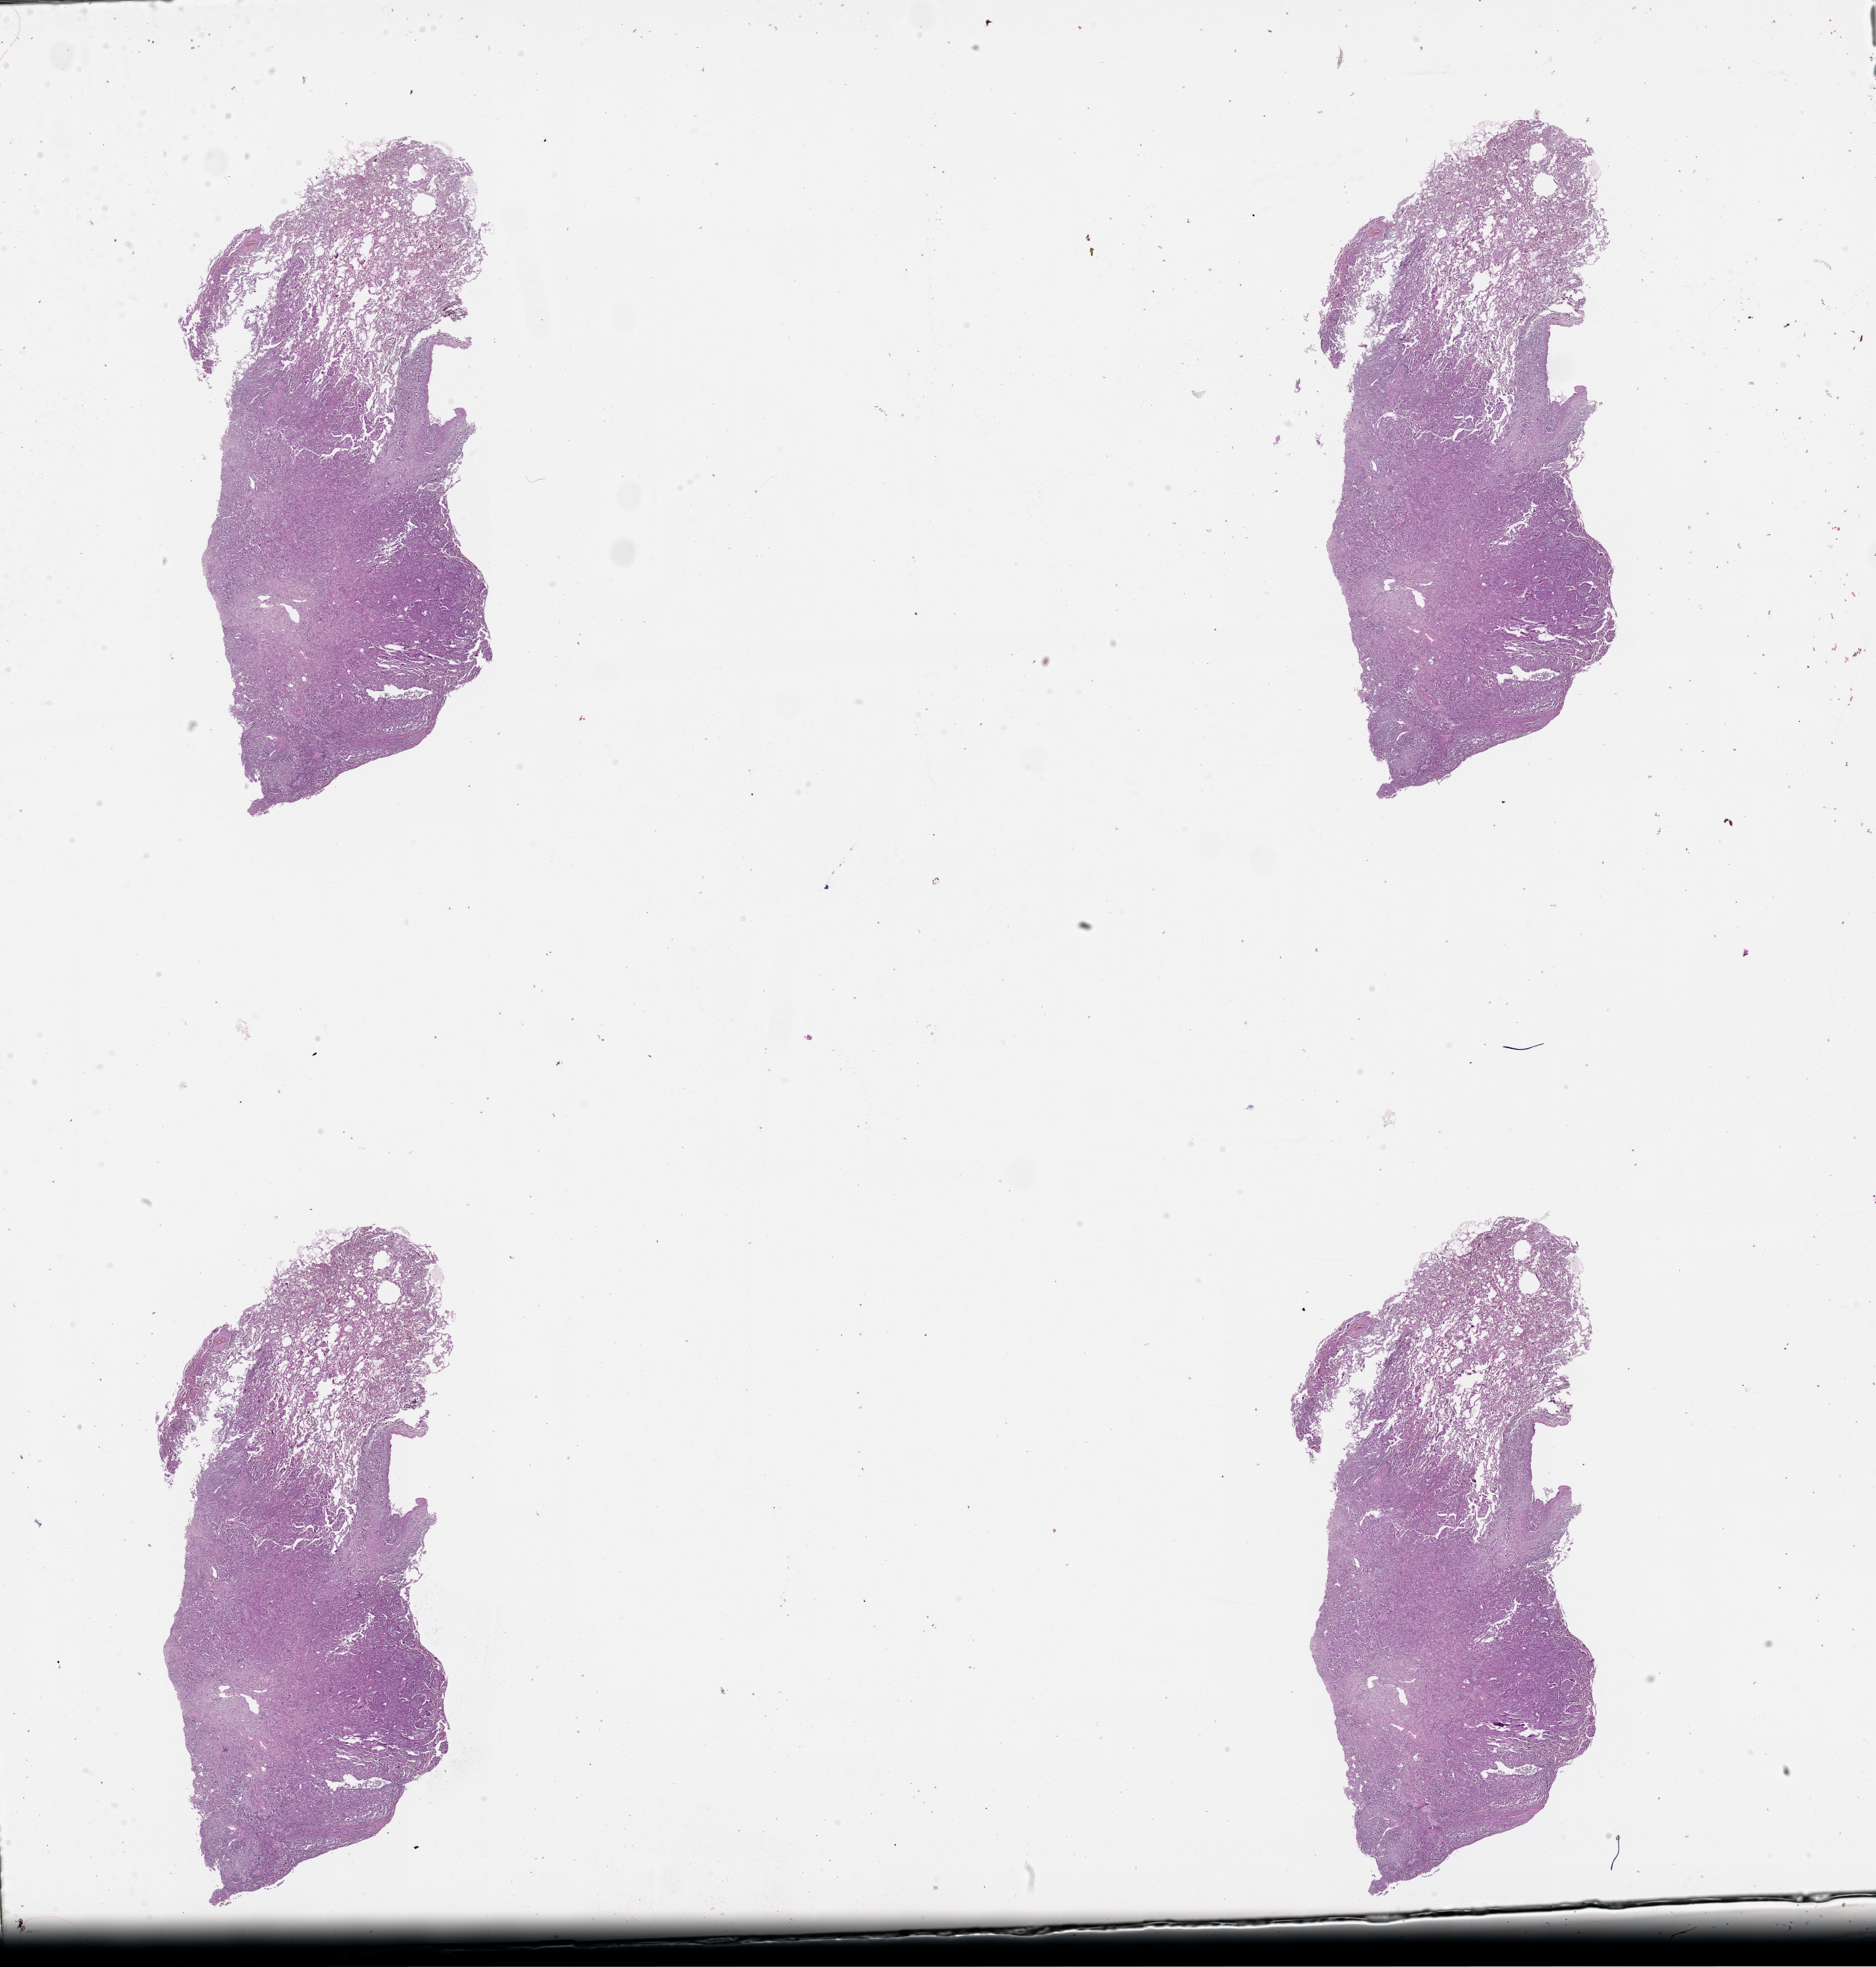
Digitized H&E-stained tissue section (whole slide) — a low-resolution overview of the entire scanned area, about 23.1 x 24.2 mm, tumour tissue sample, lung. 51-year-old female patient. Histologic grade: GX (grade cannot be assessed).
- diagnosis: Adenocarcinoma, NOS
- primary tumour site (as recorded): left lower lobe
- AJCC pathologic stage: IA